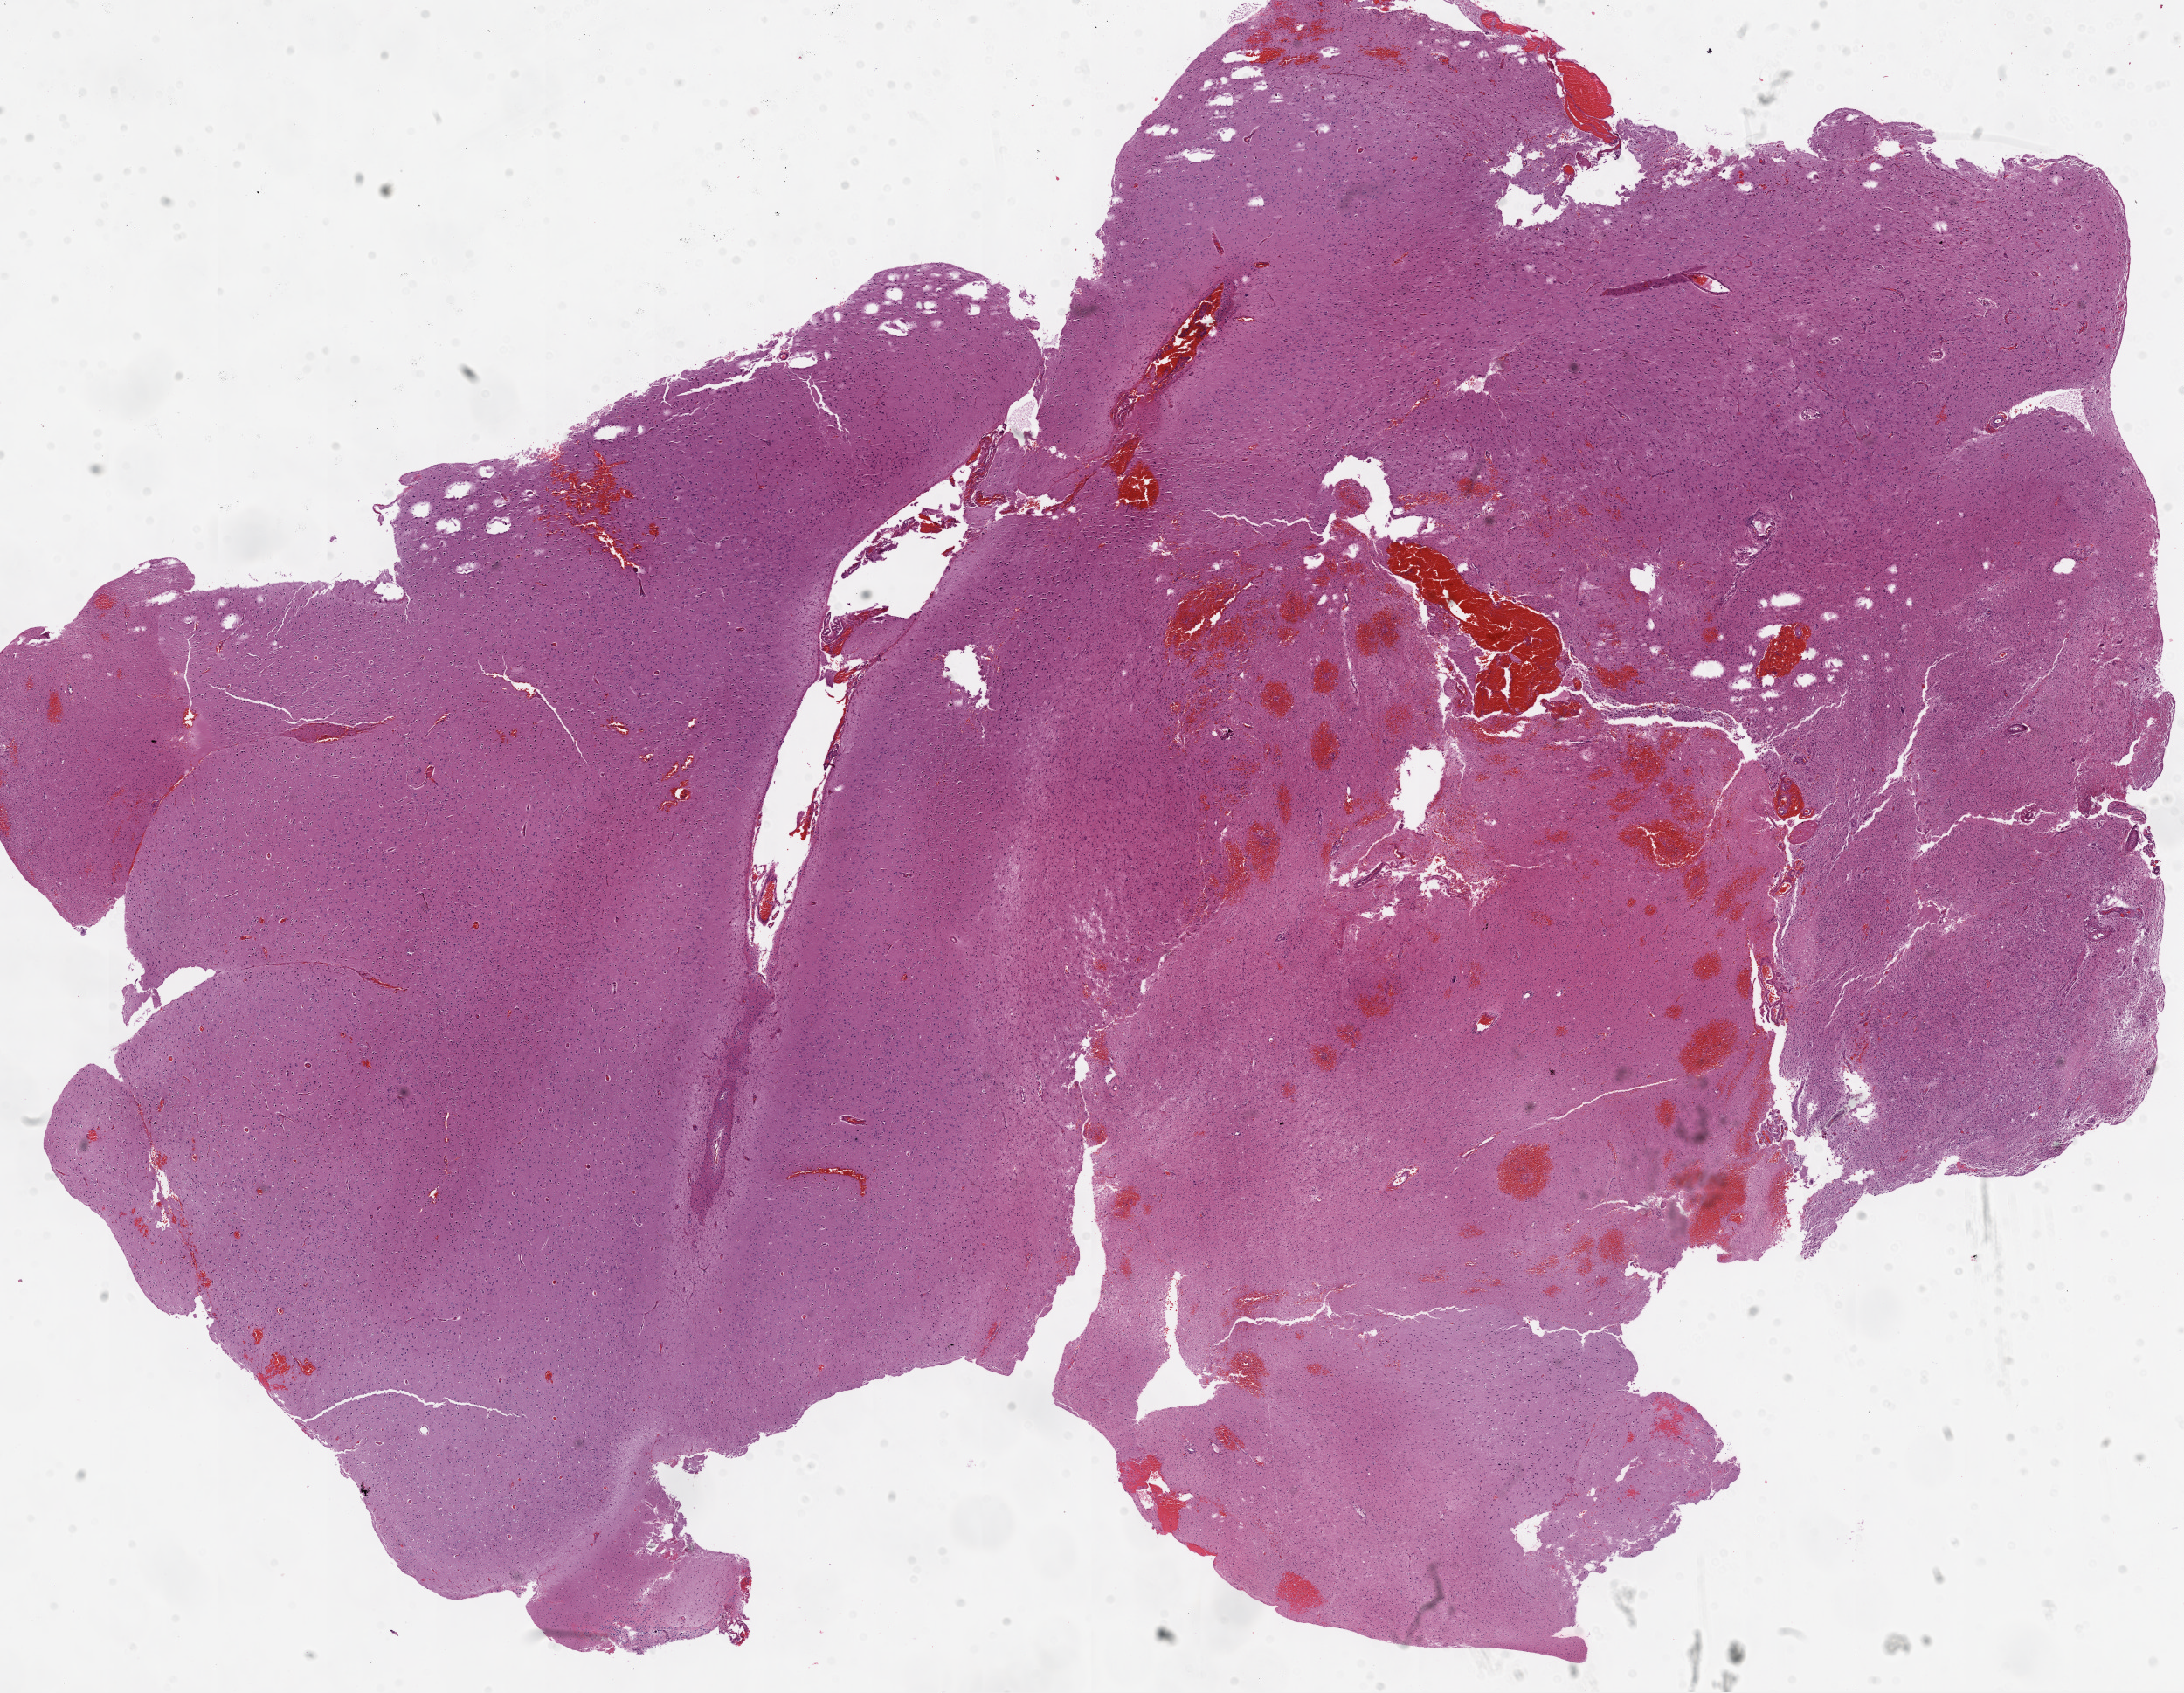
Whole-slide histology image, Hematoxylin and eosin (H&E) stained, low-resolution overview of the scanned area, about 20.1 x 15.6 mm (acquisition: 20x scan), FFPE section, primary tumour sample from the brain. Female, age 56 years at initial diagnosis.
- diagnosis: Glioblastoma